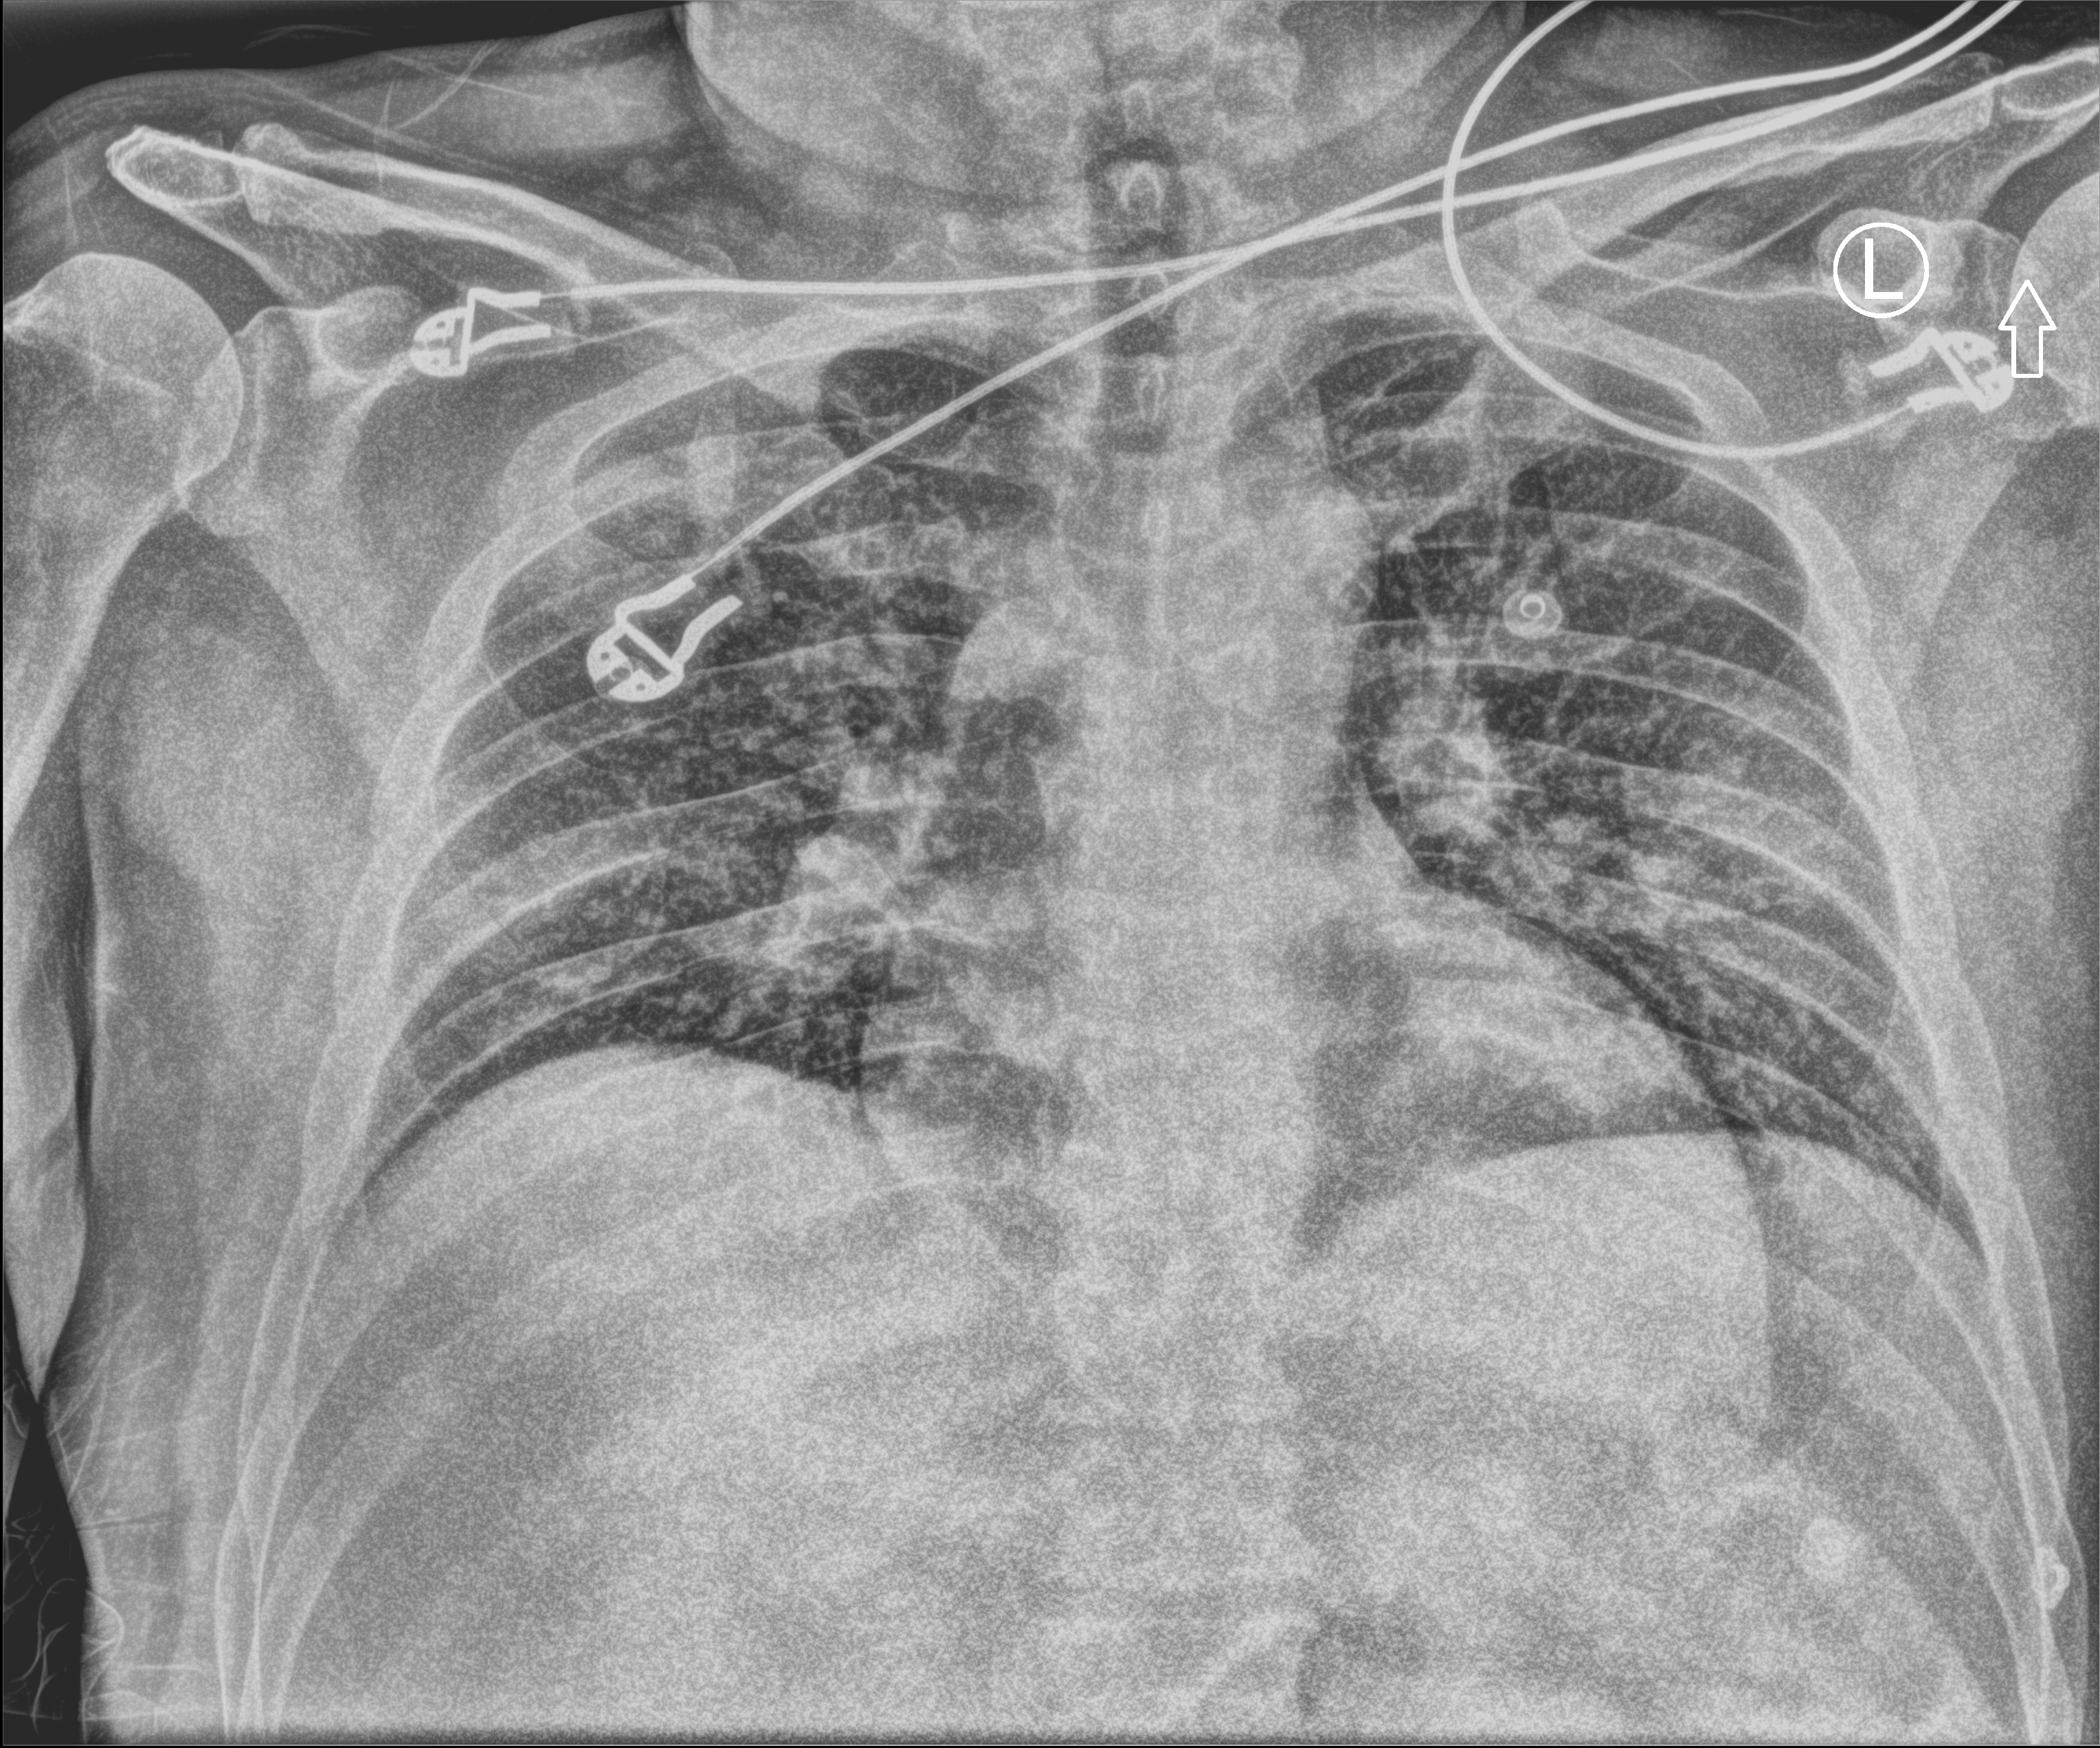
Bedside chest radiograph (computed radiography); anteroposterior (AP) projection. Patient hospitalised with COVID-19; male, aged 18–59 years.
Hospital-stay facts (about this admission, not read from this image; timing relative to this image not recorded): mechanically ventilated during this hospital stay: no; admitted to intensive care during this hospital stay: no.